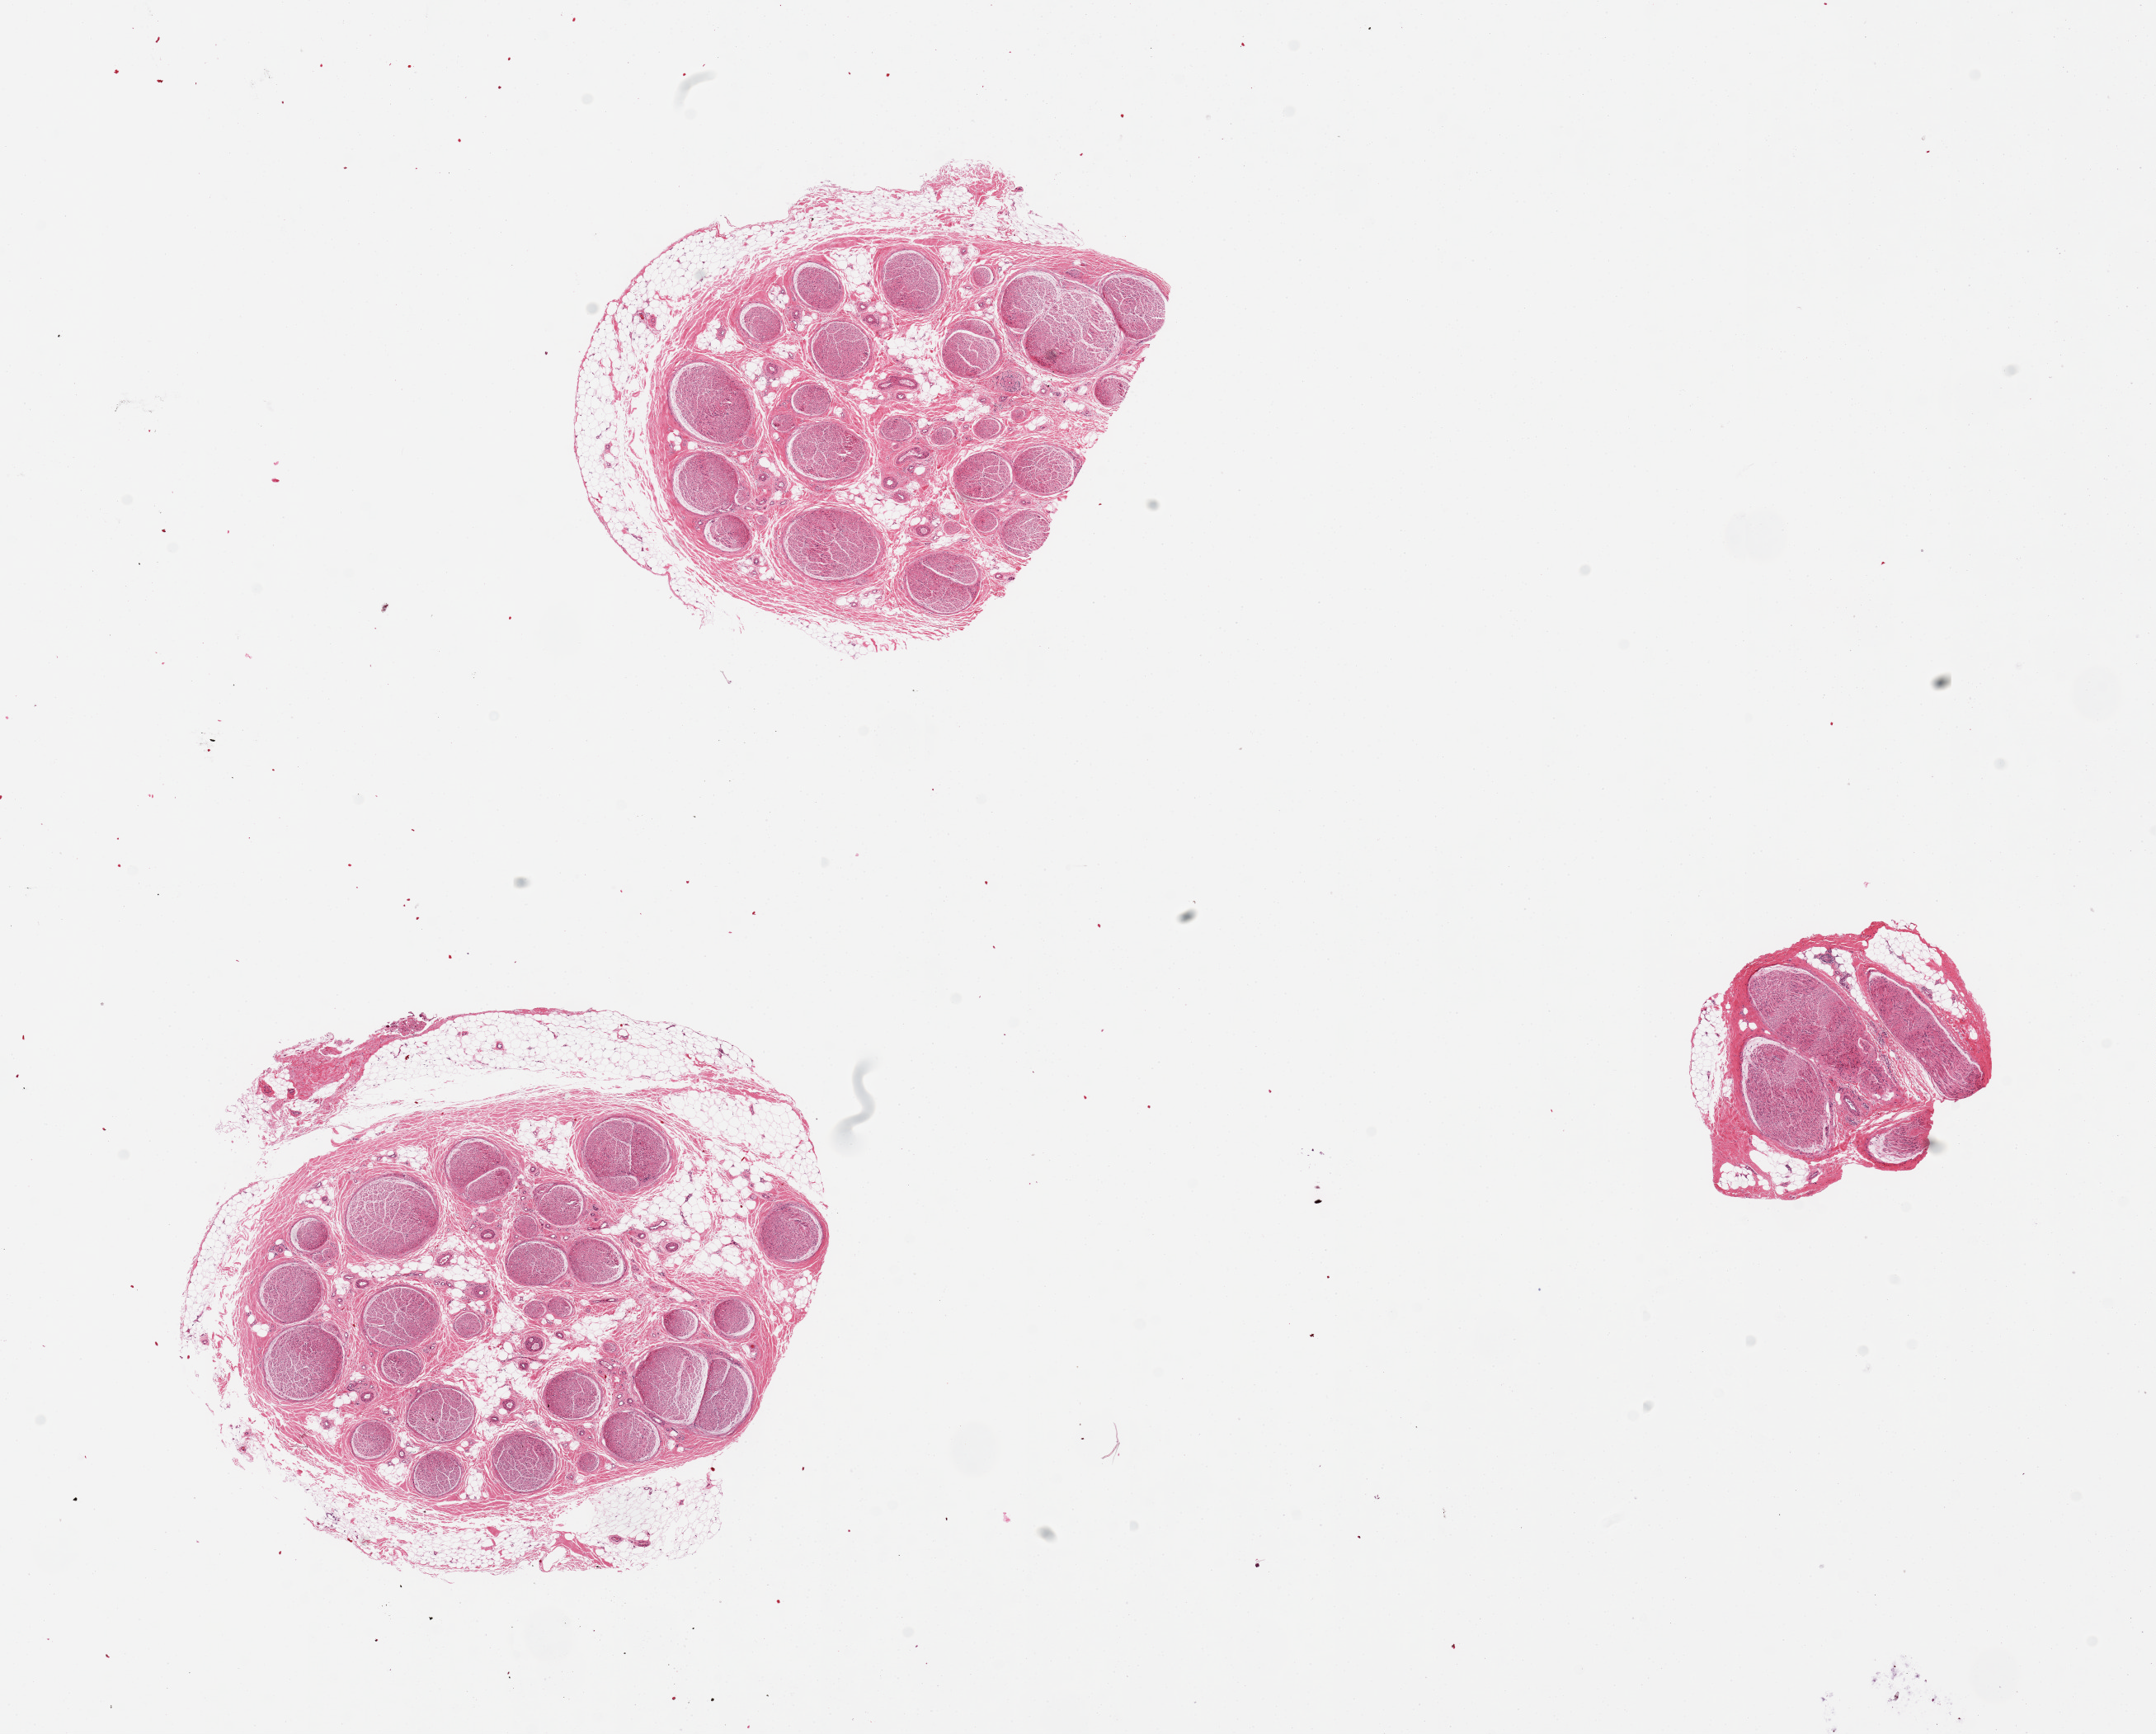
Digitized haematoxylin and eosin-stained section — a low-resolution overview of the entire scanned area, about 20.7 x 16.6 mm (from a 20x scan), PAXgene-fixed, paraffin-embedded tissue, sampled site (target tissue): tibial nerve, tissue donor sample. Female donor.
Pathologist's review note for this sample: 3 pieces, discontinuous rim of fat, up to ~1mm.